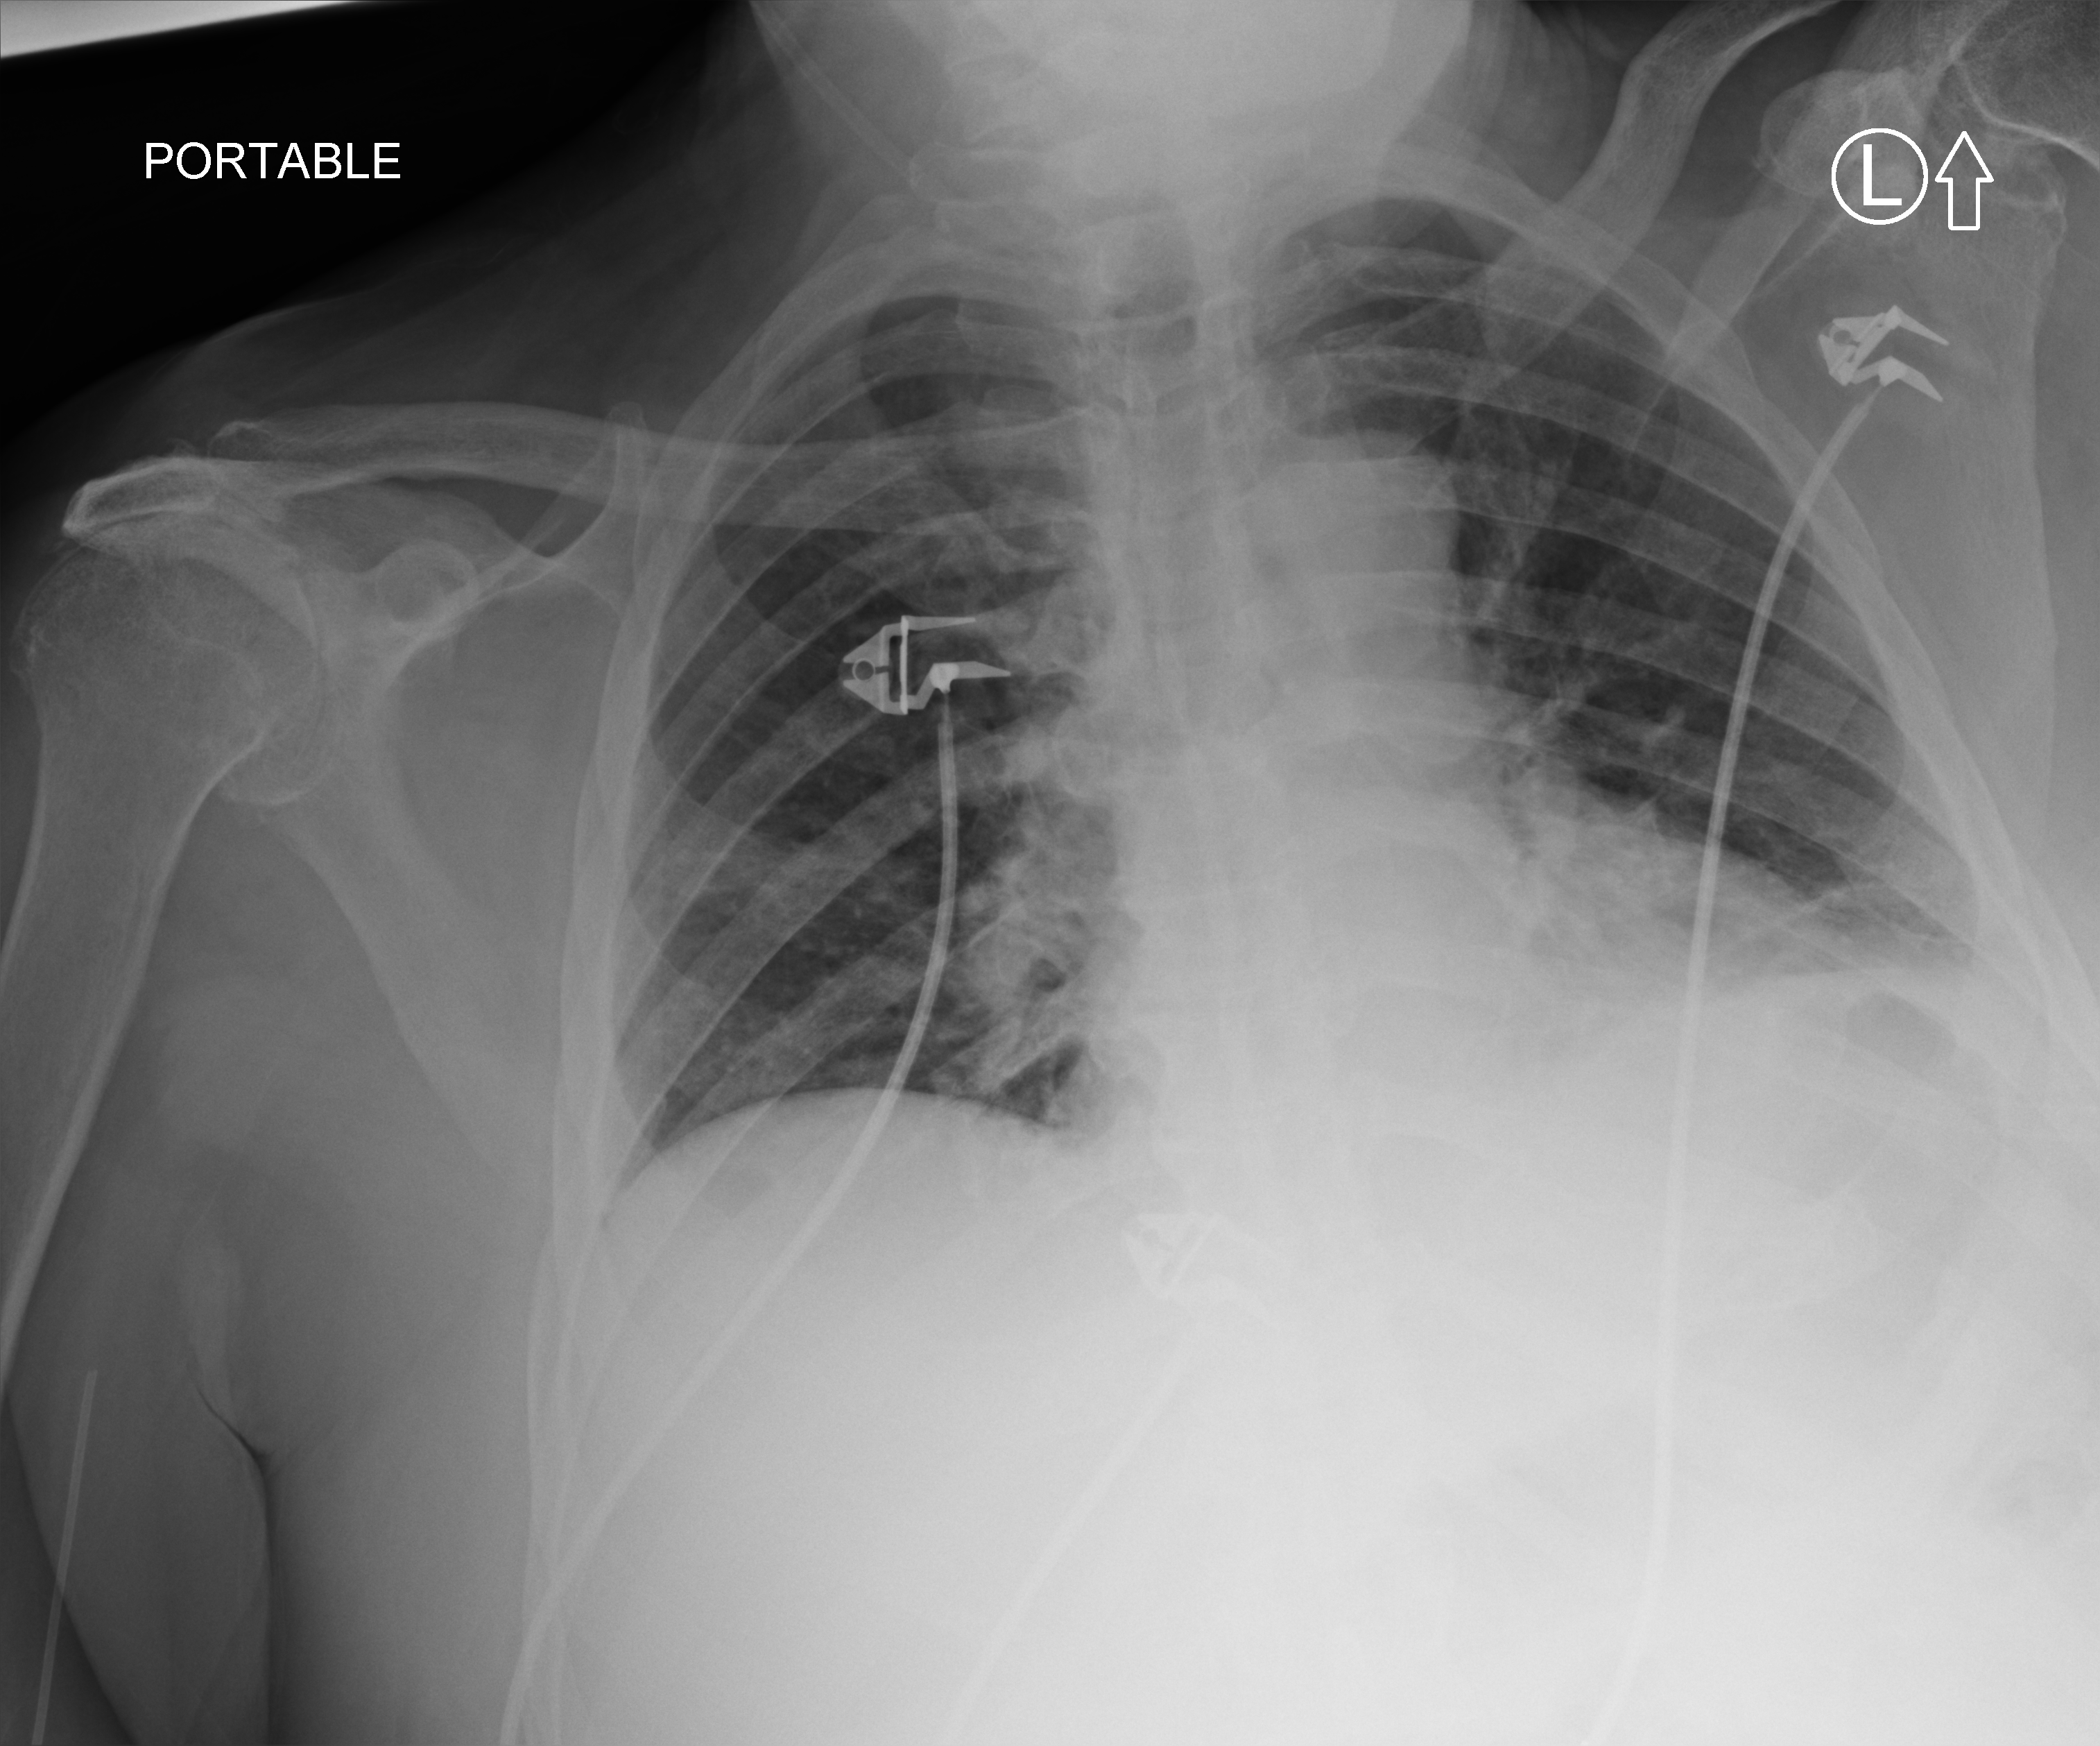
Chest X-ray (portable). Male patient hospitalised with COVID-19, age 75–90 years.
Admission-level facts for this patient (not findings on this image; timing relative to this image not recorded): admitted to intensive care during this hospital stay: yes; length of hospital stay: 12 days.